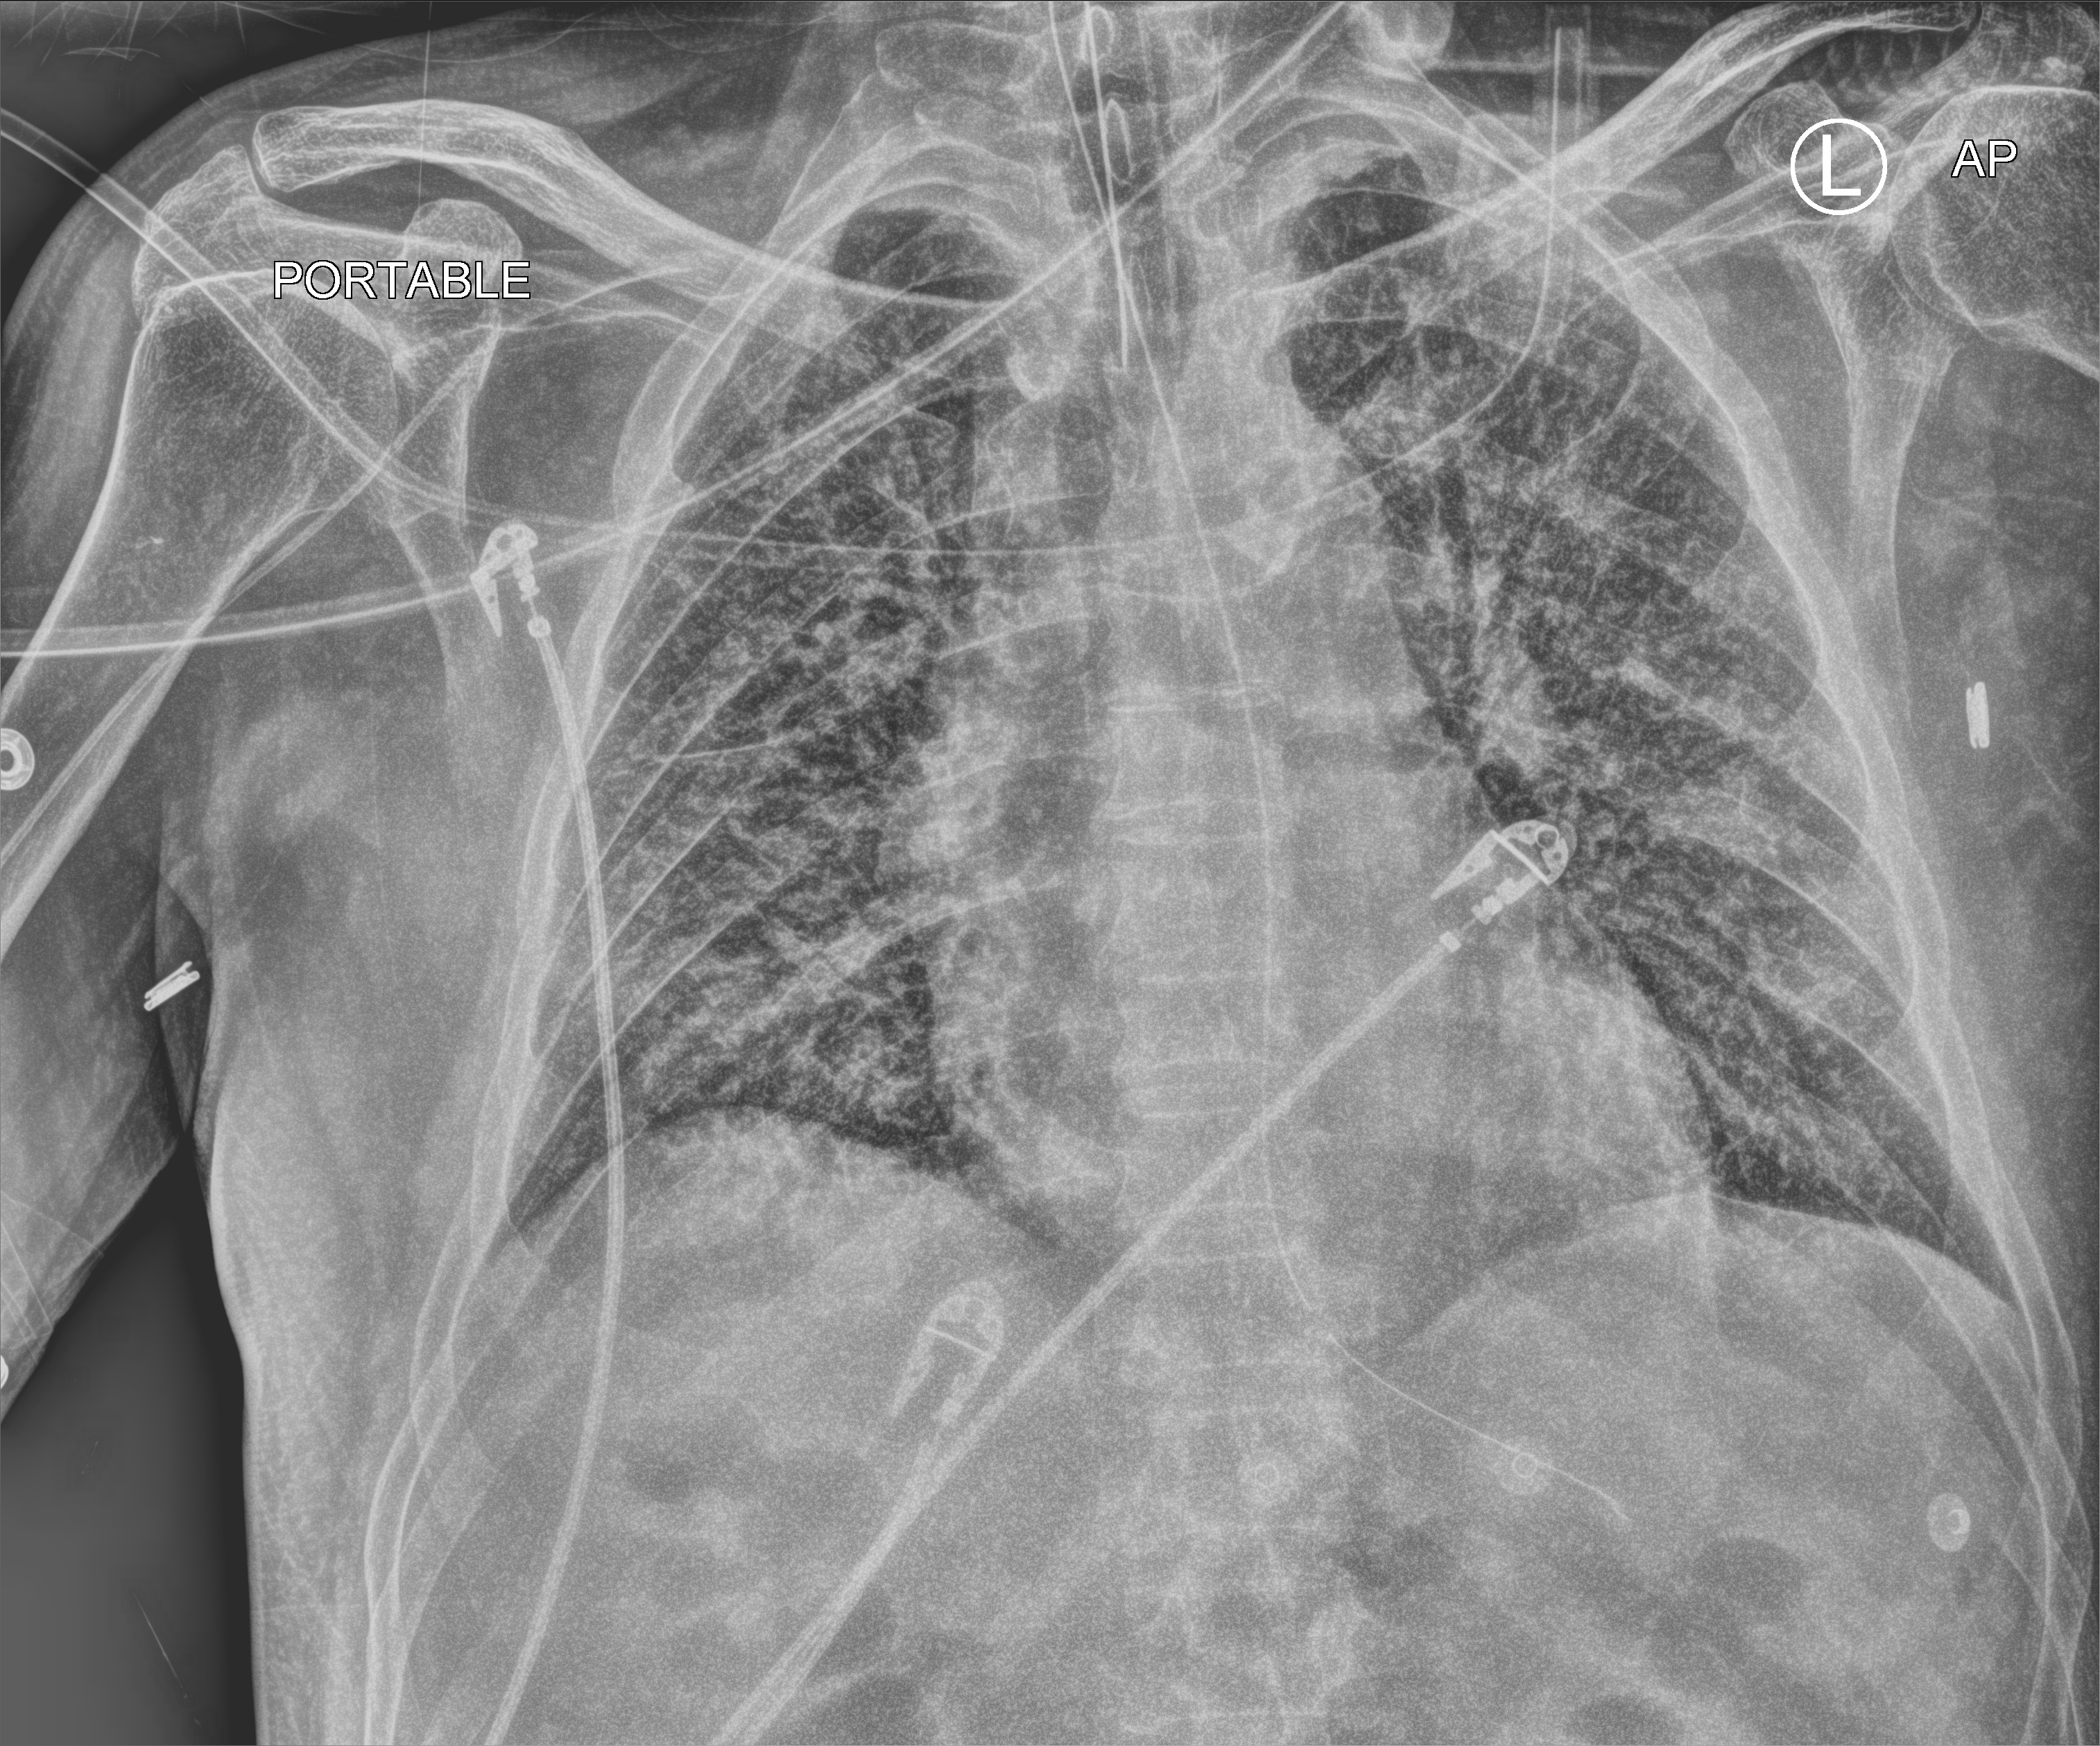
Portable chest radiograph, anteroposterior (AP) projection. Patient hospitalised with COVID-19; male, aged 60–74 years.
Admission-level facts for this patient (not findings on this image; timing relative to this image not recorded):
- COPD (admission record): no